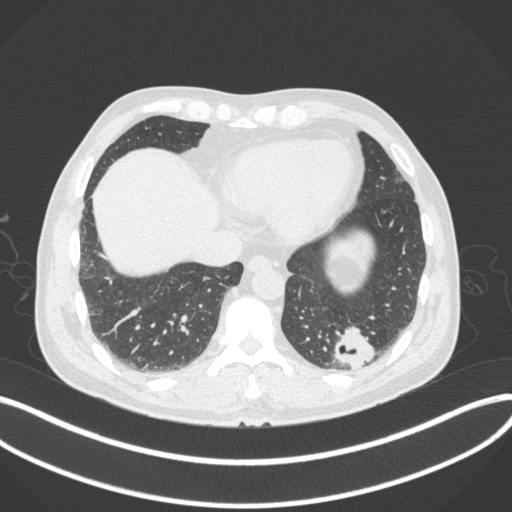
Chest CT, one axial slice. Position 68 of 313 along the scan axis. Reconstruction kernel B31f. Lung window (W 1500 / L -600 HU). 1 mm slice thickness. 512 × 512 image matrix. Patient: male, 54 years. From the clinical record (not read from this slice): clinical TNM (as recorded): T1c N0 M1; histopathological grade: G3.
Outlined on this slice (rectangle marked by the reading radiologist):
- lung tumour (recorded histology: adenocarcinoma): bounding box <332,319,377,372> (left, top, right, bottom; pixels)